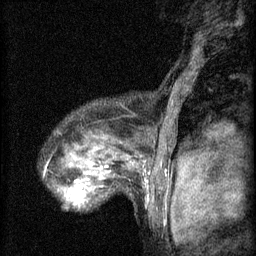
Breast MRI (dynamic contrast-enhanced), one sagittal slice; slice 49 of 60 in the series (ordered by position); 3 images stored at this slice position (order not interpretable as contrast timing); 1.5 T; TE 4.2 ms, TR 8.2 ms; 2 mm slice thickness; 256 × 256 image matrix, field of view 180 × 180 mm. Patient: female, 48 years.
Outlined on this slice (semi-automatic segmentation, software-assisted and operator-edited):
- analysis volume of interest (the breast-tissue region the enhancement analysis was run in; not a lesion): bounding box (x1, y1, x2, y2) in pixels: (58, 160, 113, 207)
- tumour enhancement mask (voxels above the 70 % enhancement threshold inside the analysis volume of interest): (69, 176, 103, 203)